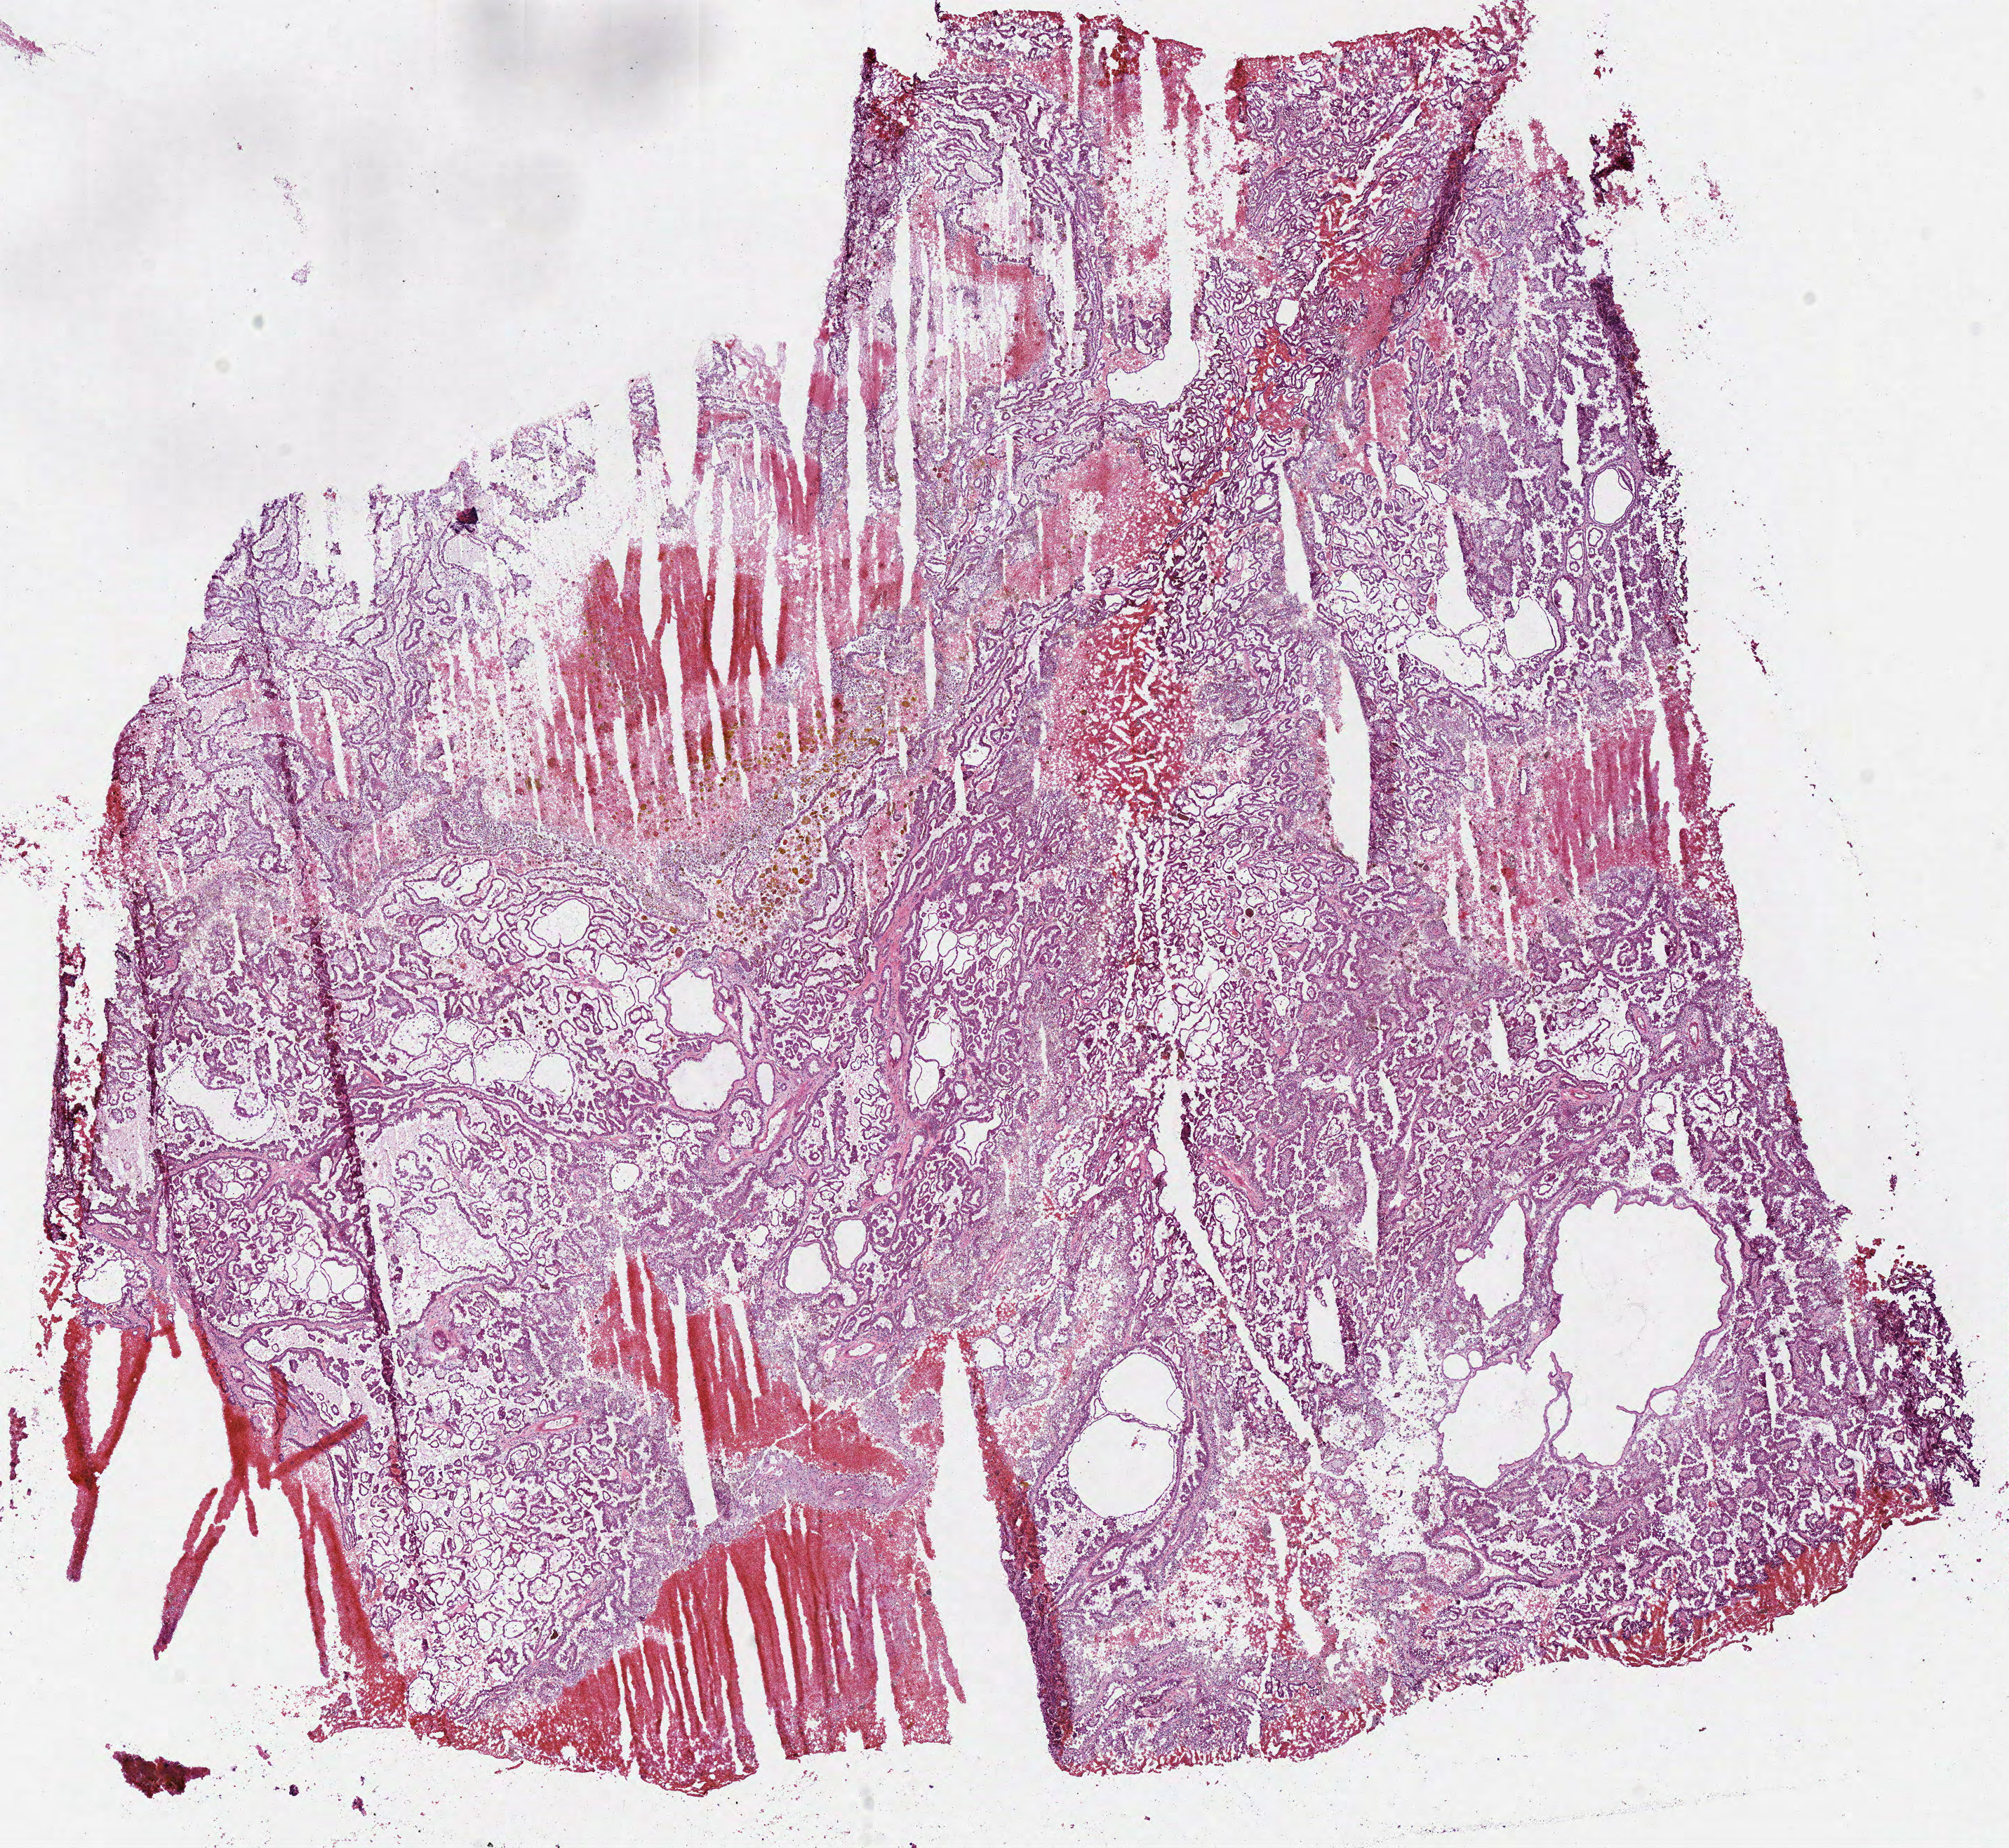
Whole-slide histology image, H&E-stained — shown as a low-resolution overview of the whole scanned area (about 11.3 x 10.4 mm, acquisition: 40x scan), frozen section from the bottom of the tissue portion, kidney, primary tumour sample. Patient: male, age at initial diagnosis 57 years. Slide review estimates, as recorded: tumour cells 81%, tumour nuclei 85%, normal cells 0%, stromal cells 1%, necrosis 18%.
Laterality: right. Pathologic diagnosis: Papillary adenocarcinoma, NOS. TNM: T1a NX MX. AJCC pathologic stage: I (6th edition).